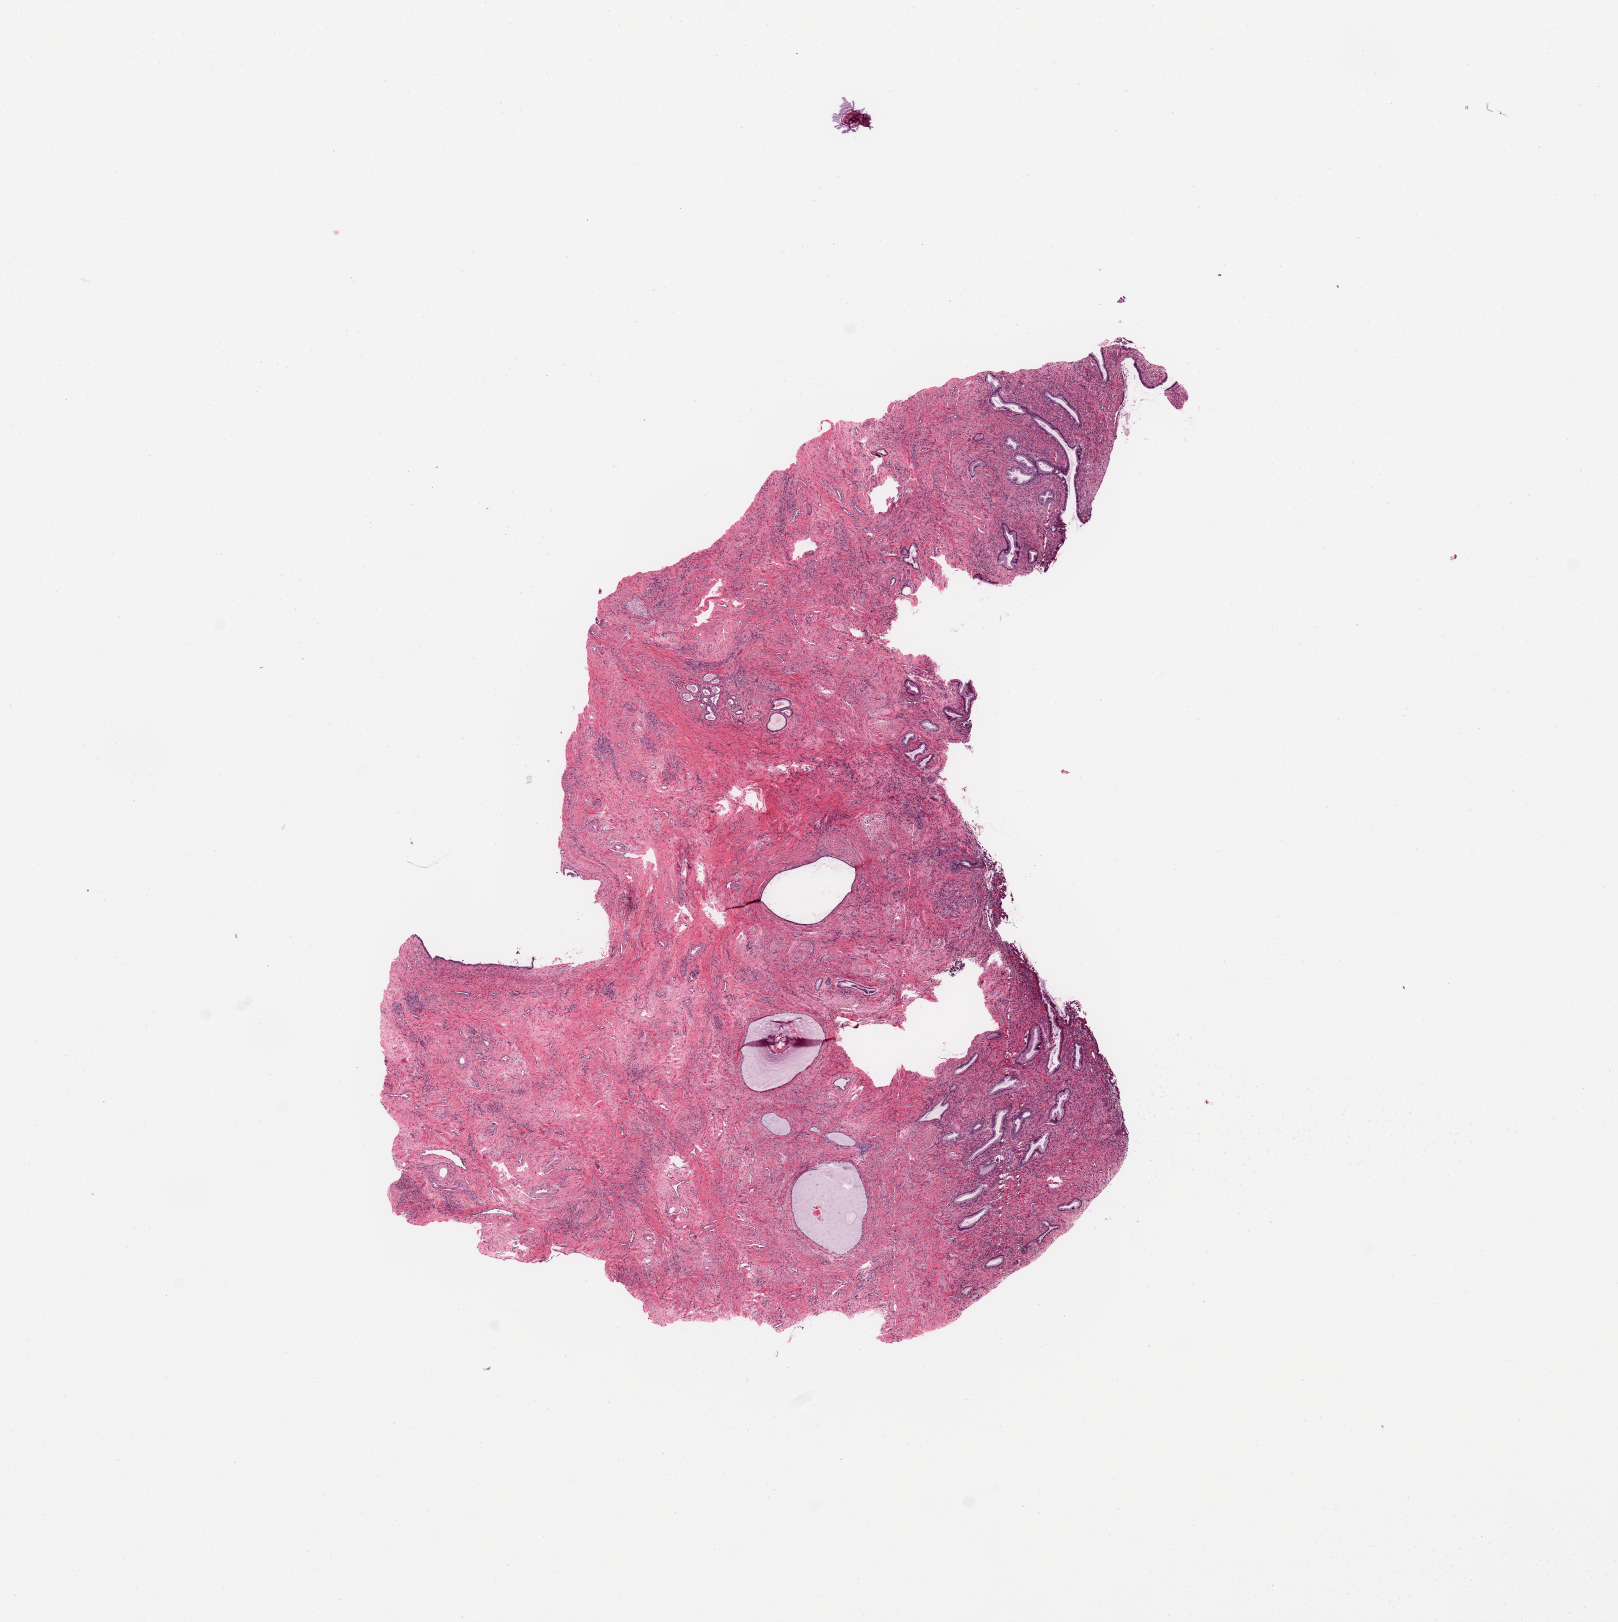
Digitized H&E tissue section (whole slide), whole scanned area (about 12.8 x 12.8 mm, from a 20x scan) shown as a low-resolution overview, normal (non-tumour) tissue sample, sampled site: uterus. 68-year-old female patient.
- this section: normal (non-tumour) tissue from the same patient
- patient diagnosis: Endometrioid adenocarcinoma, NOS